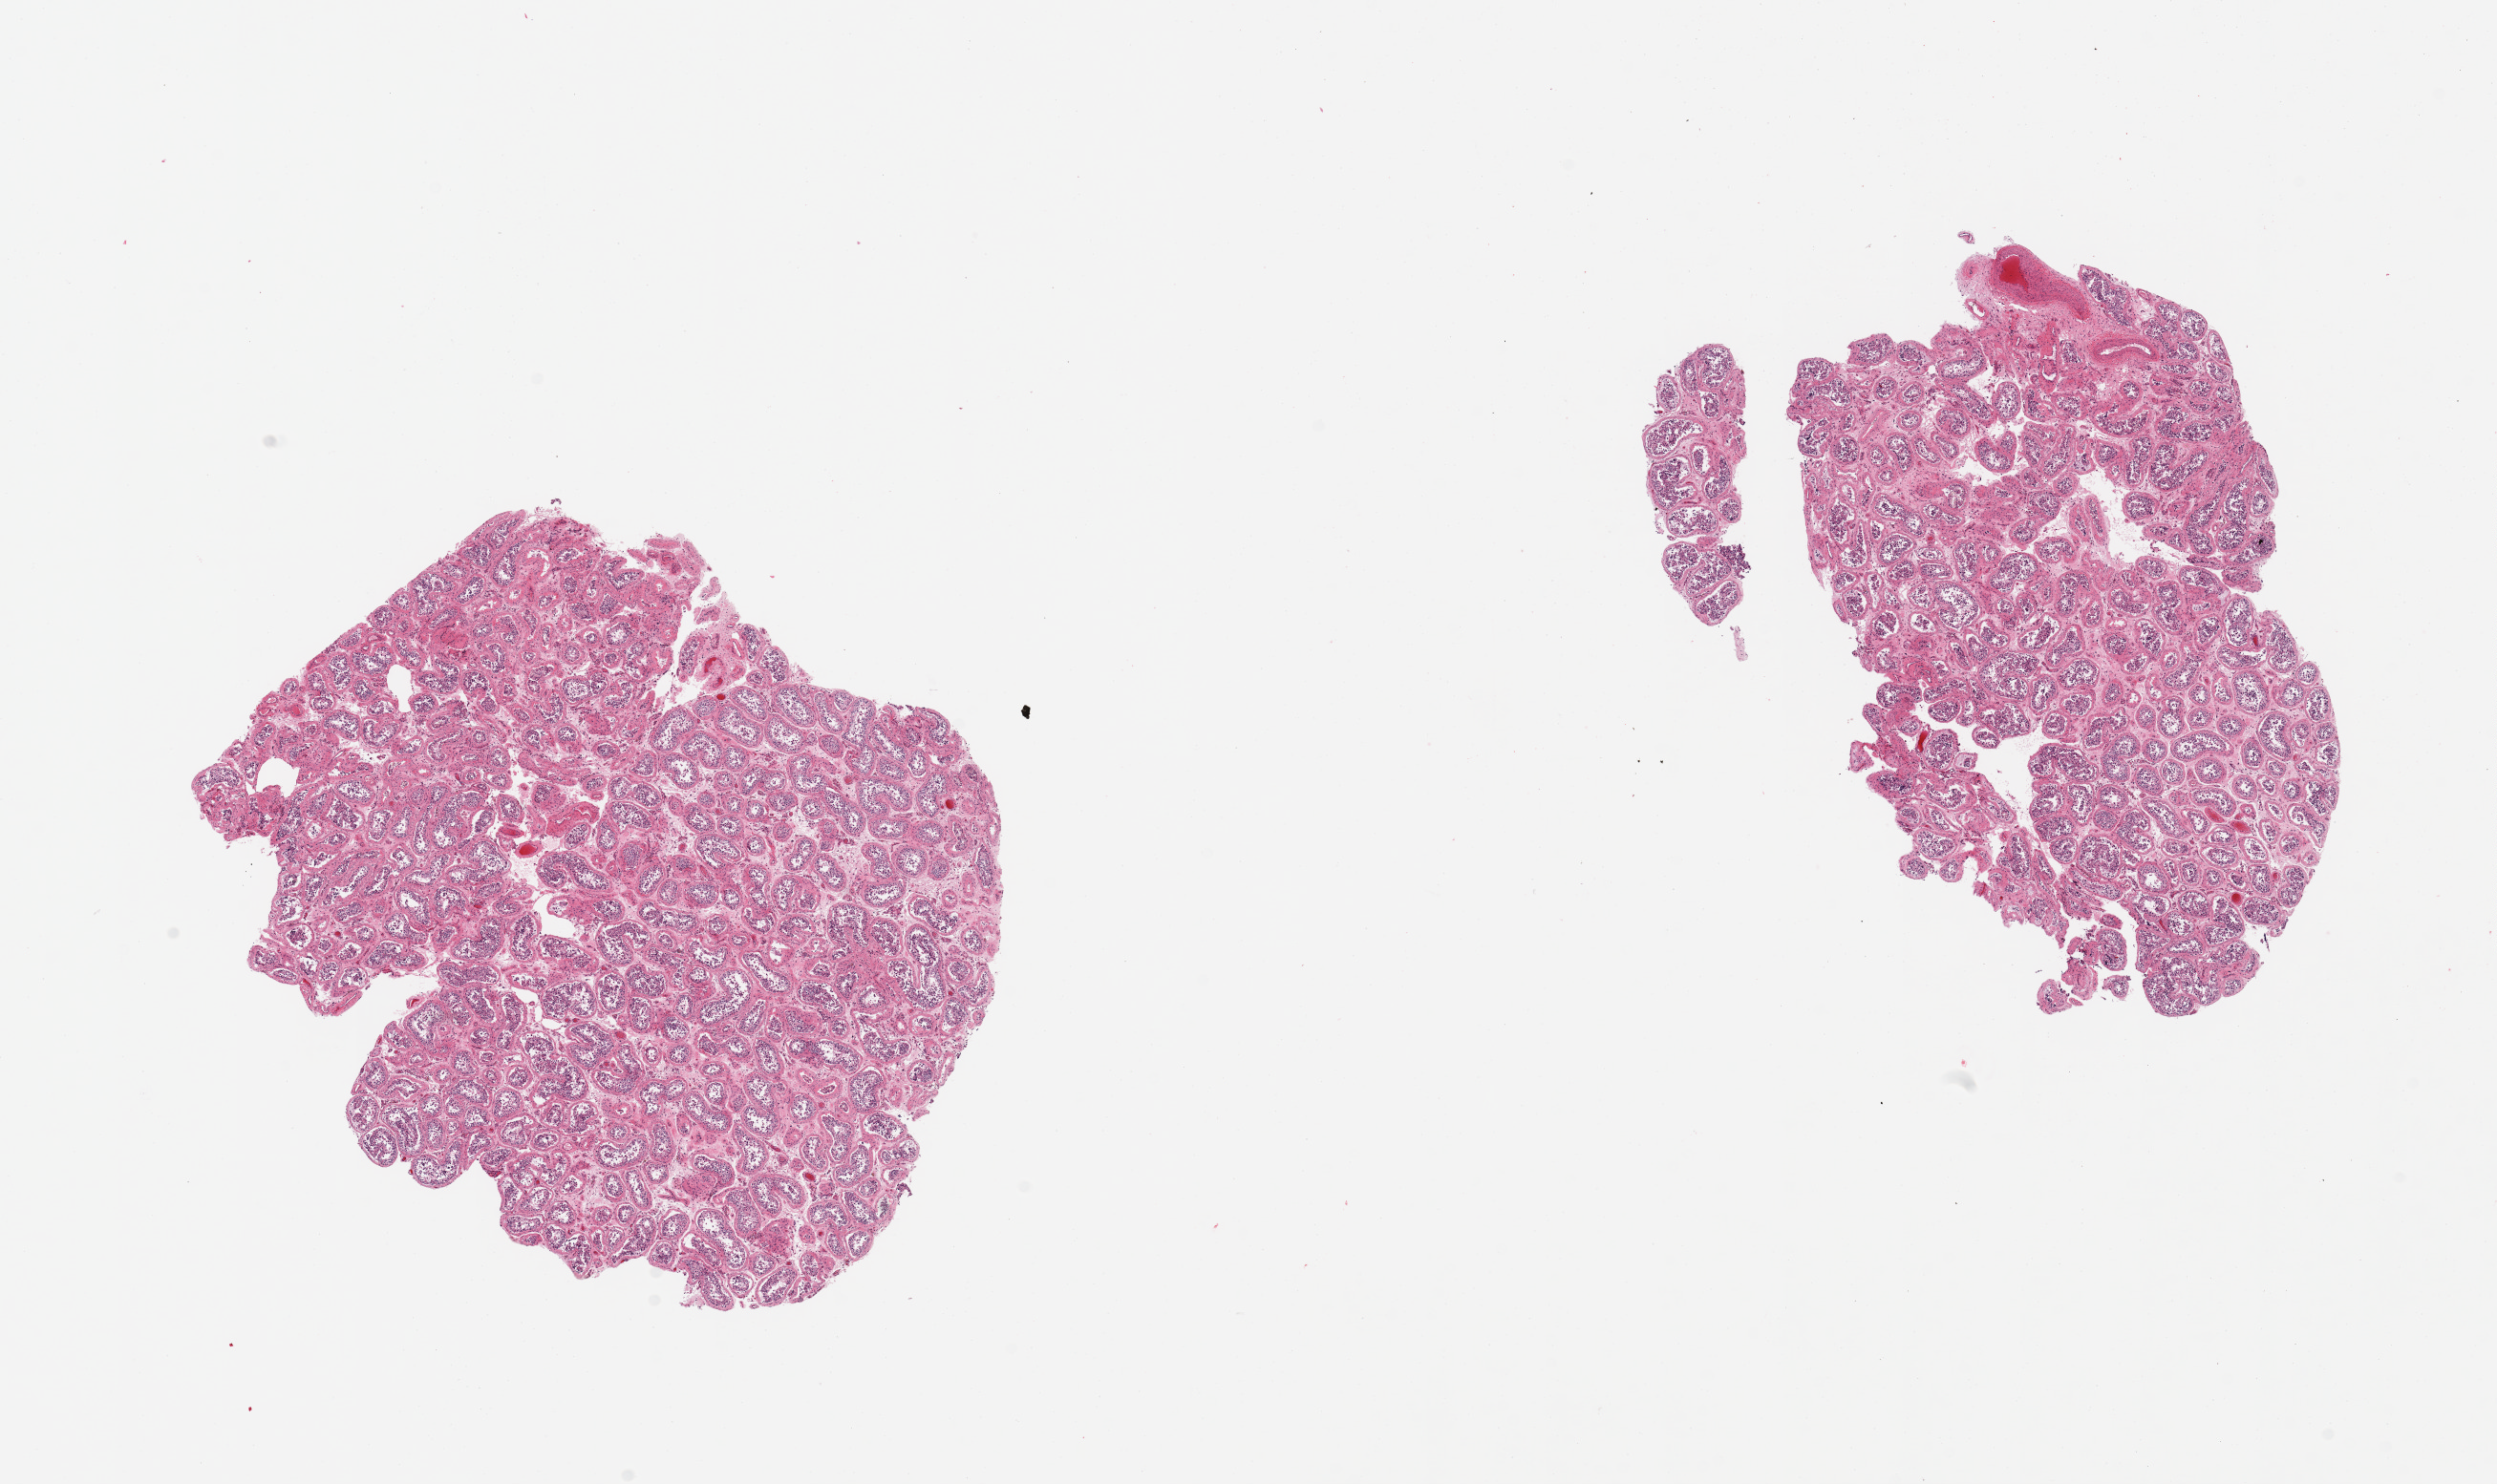
Whole-slide image, hematoxylin and eosin (H&E) stain, whole scanned area (about 20.7 x 12.3 mm, from a 20x scan) shown as a low-resolution overview; PAXgene-fixed paraffin-embedded (PFPE) section; target tissue: testis; tissue donor sample. Donor: male.
• reviewer comment on this tissue sample: 2 pieces, spermatogenesis appears reduced